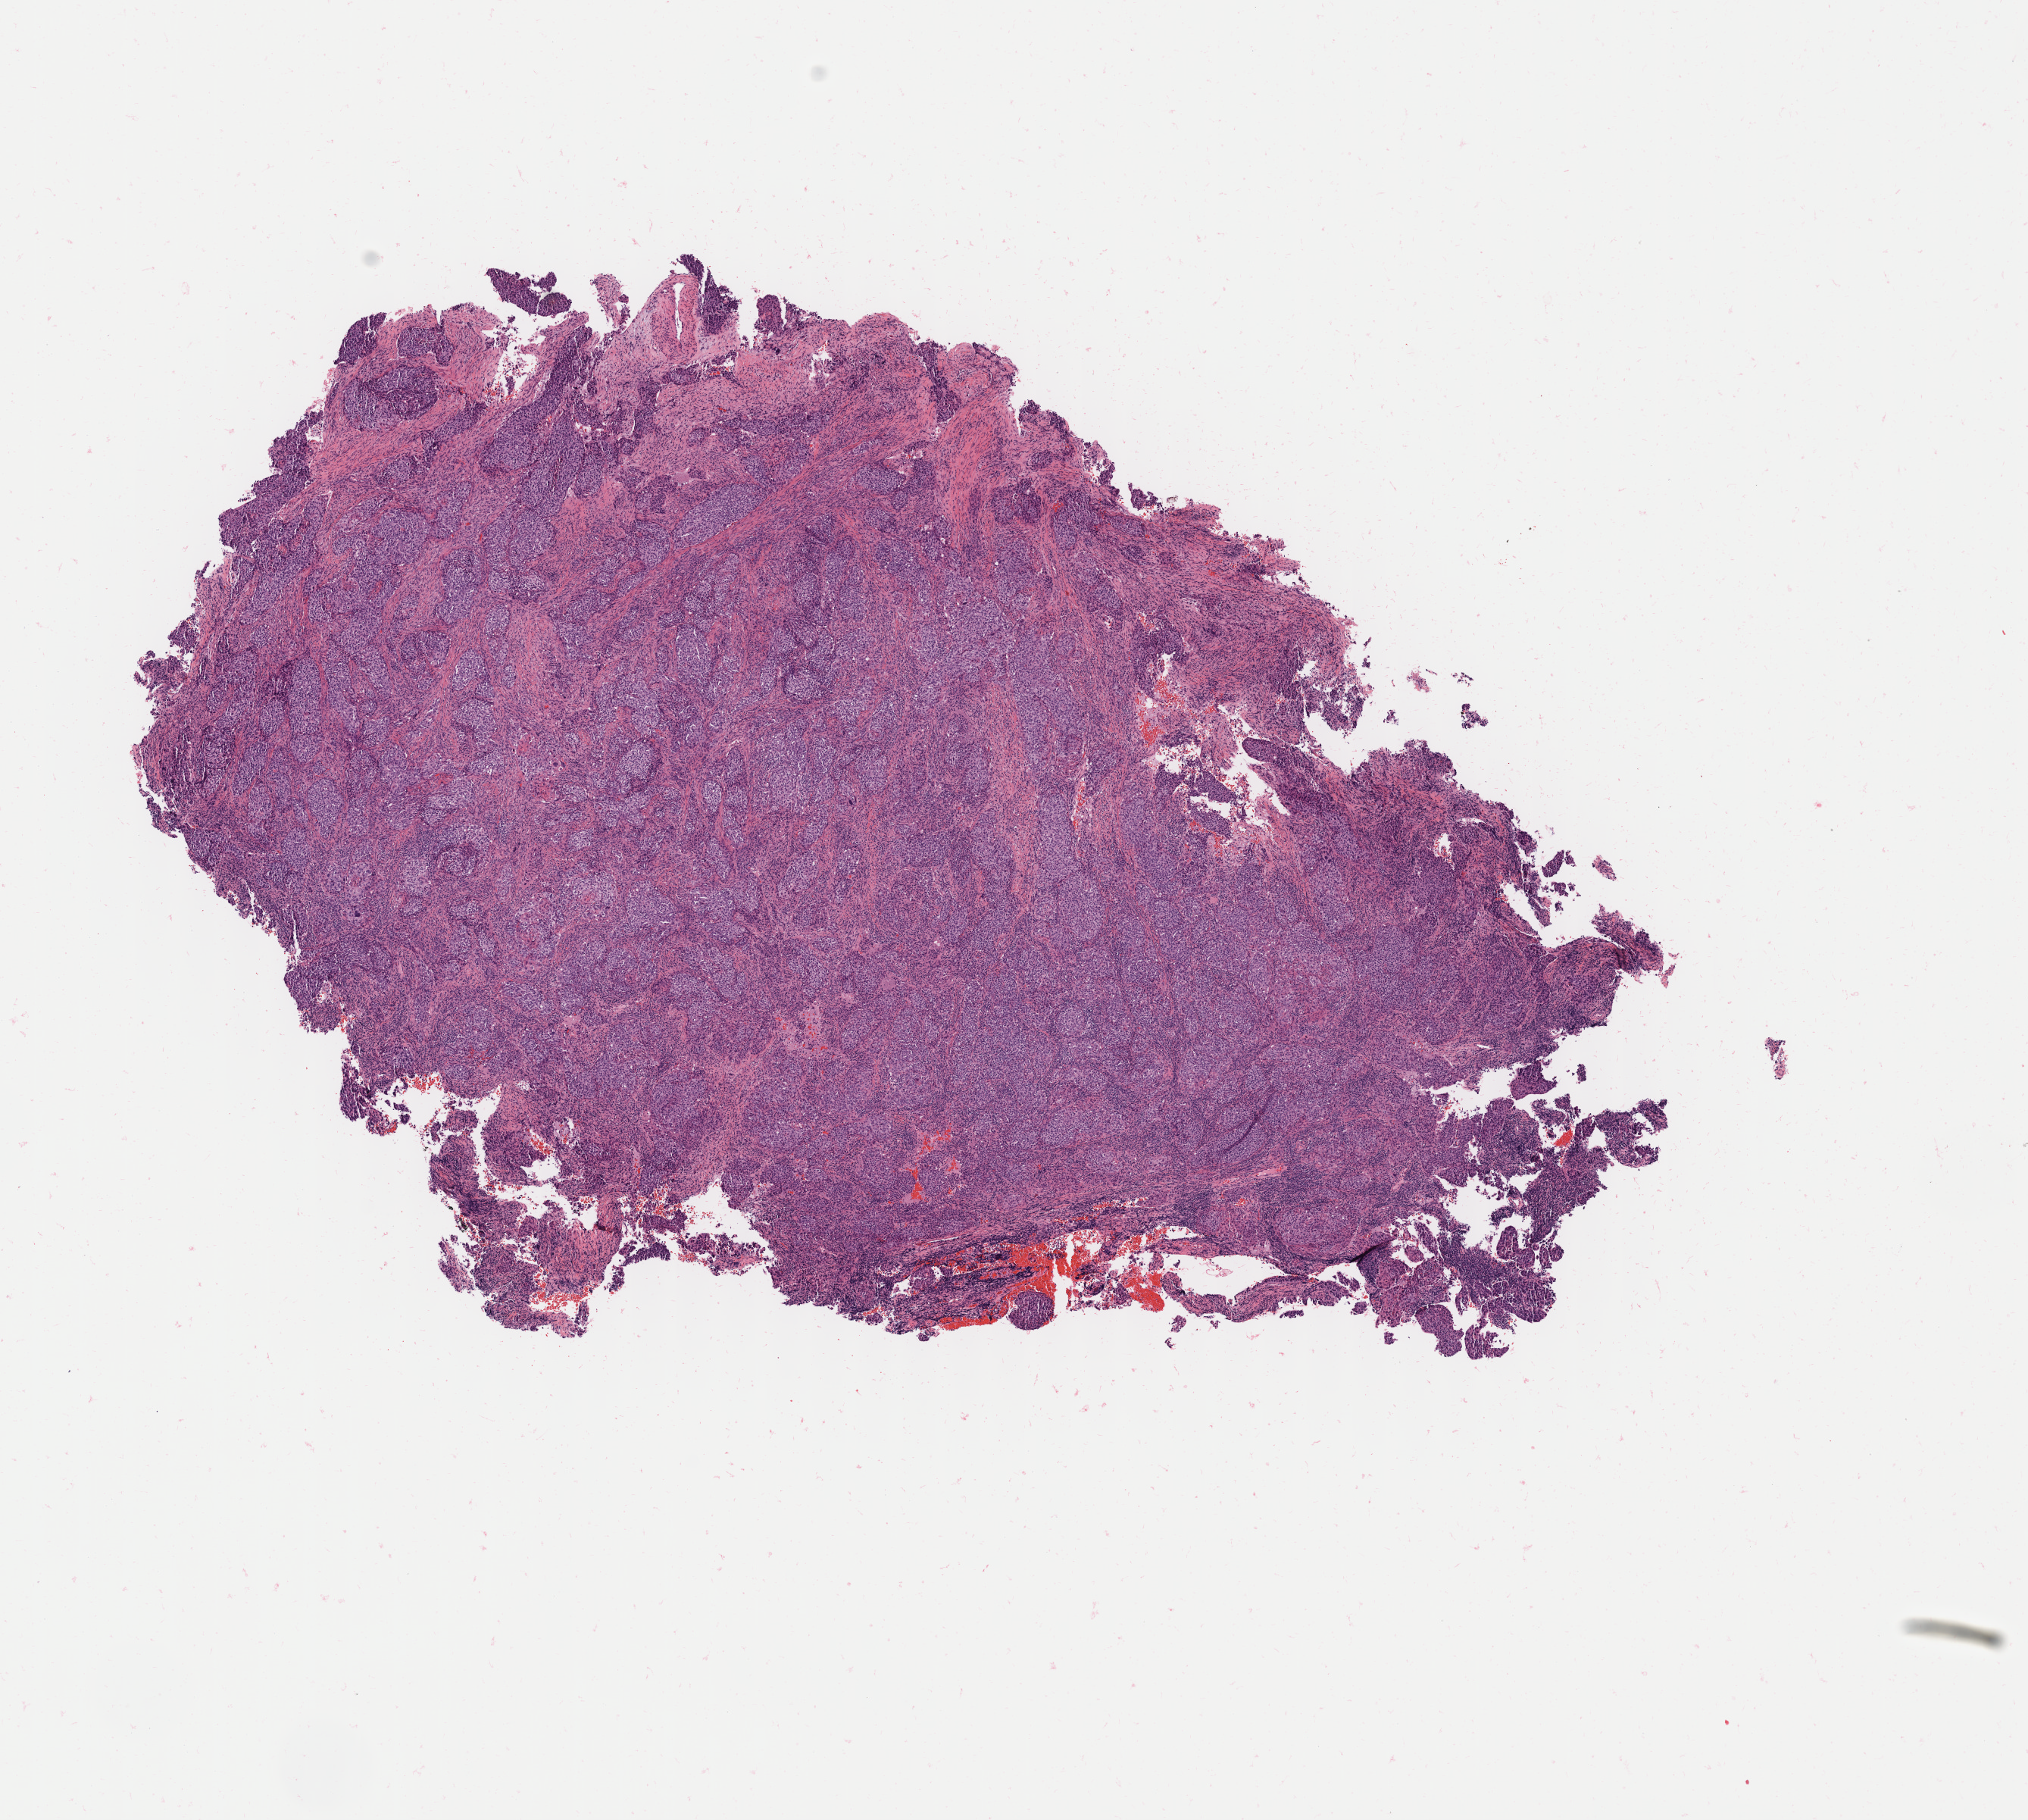
Digitized hematoxylin and eosin (H&E)-stained section, a low-resolution overview of the entire scanned area, about 10.7 x 9.6 mm. Specimen: tumor tissue. Site: cervix. Female patient, age 51 years.
Diagnosis: Squamous cell carcinoma, large cell, nonkeratinizing, NOS.